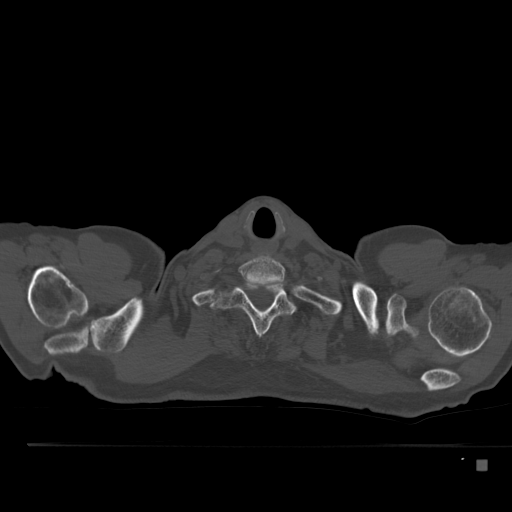
CT including the spine, one axial slice; position 428 of 517 along the scan axis; reconstruction kernel Br40s; bone window (W 1800 / L 400 HU); 512 × 512 image matrix, field of view 408 × 408 mm. Male patient, age 70 years. From the clinical record (not read from this slice): primary cancer: renal; vertebrae with lytic lesions (as recorded): T4, T6, T10, T12, L3, L4, L5.
Structures marked on this image (semi-automatically segmented with operator editing):
- T1 vertebra: bounding box [x1, y1, x2, y2] px = [212, 282, 294, 335]